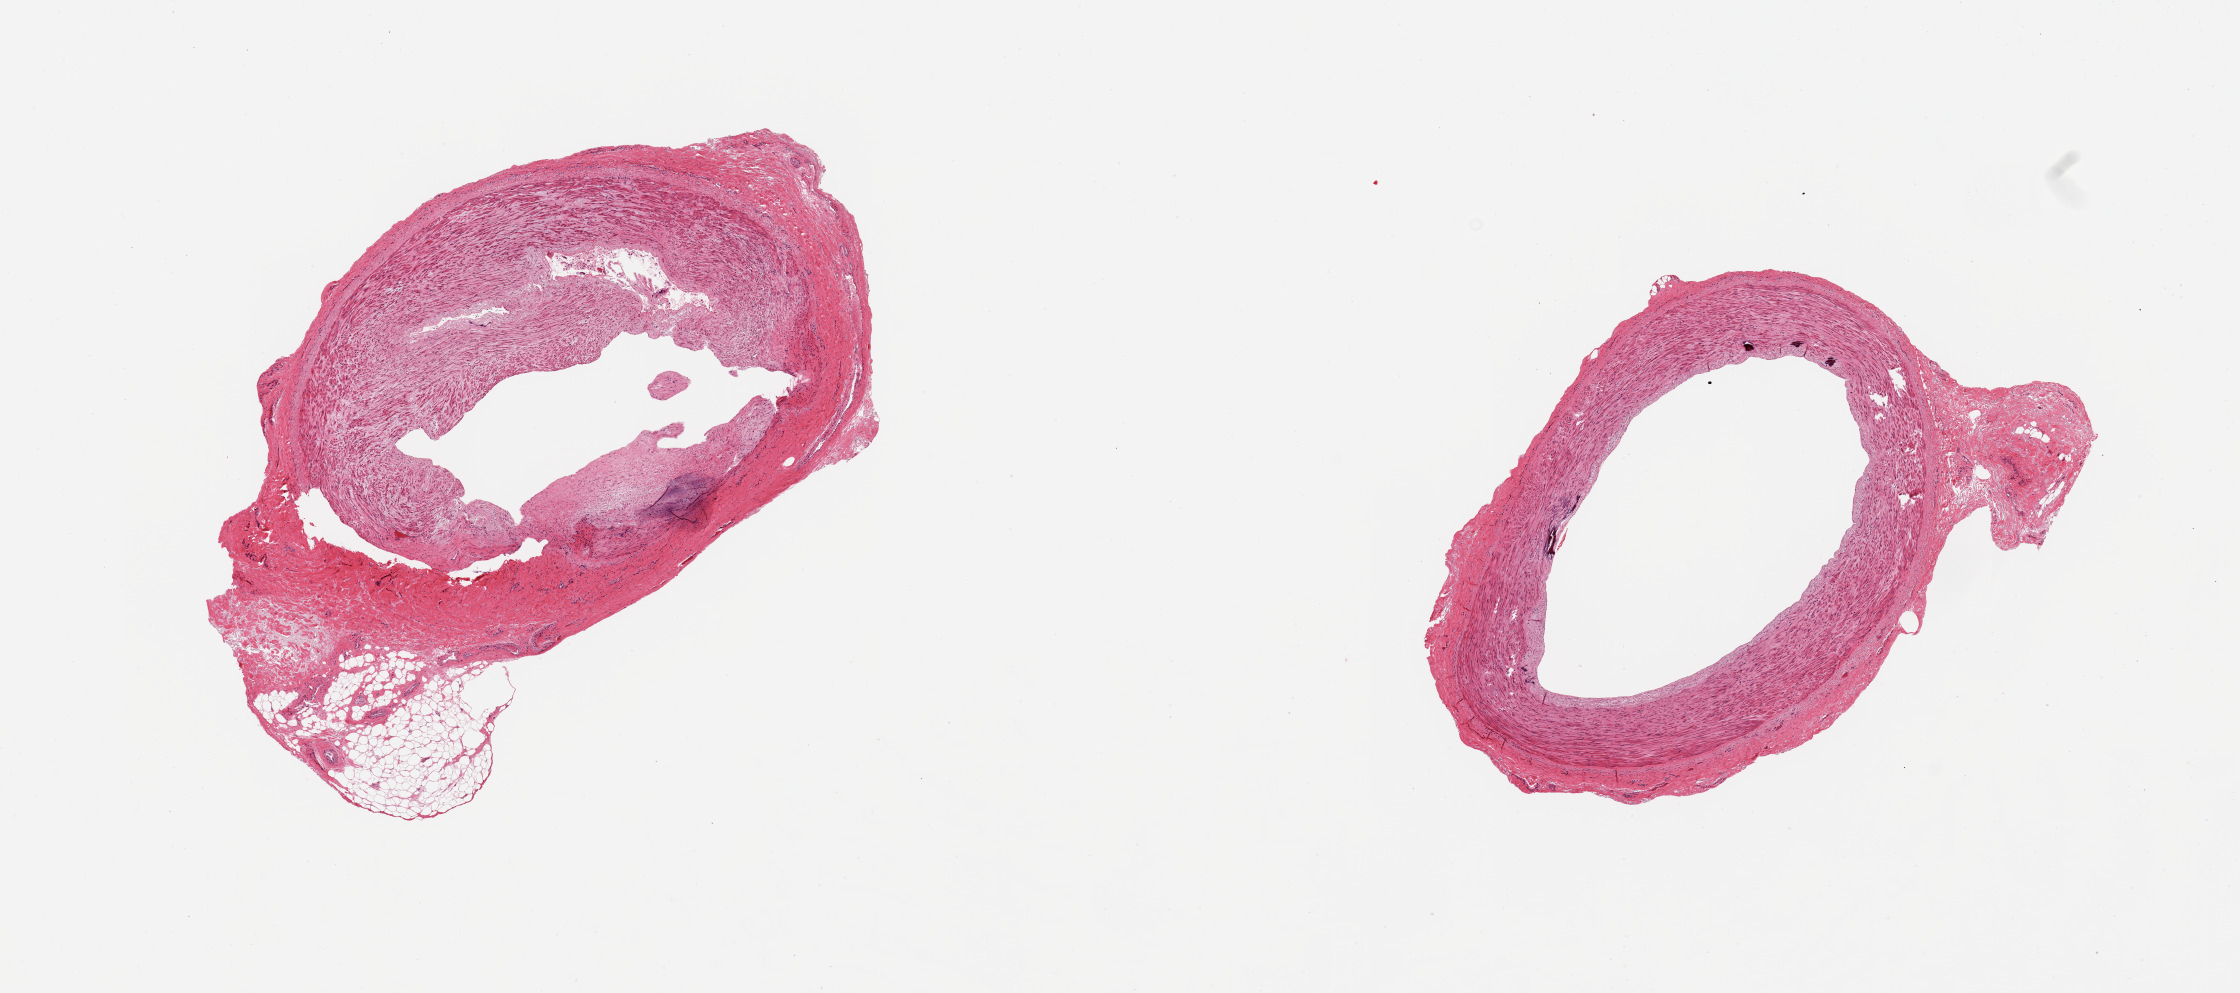
Digitized hematoxylin and eosin (H&E)-stained section, brightfield — shown as a low-resolution overview of the whole scanned area (about 17.7 x 7.9 mm), PAXgene-fixed paraffin-embedded (PFPE) section, sampled site (target tissue): tibial artery, tissue donor sample.
Reviewer comment on this tissue sample: 2 pieces; ? orientation, intimal thickening and atherosclerosis with few scattered minute calcium deposits, 1.37mm attached fat.